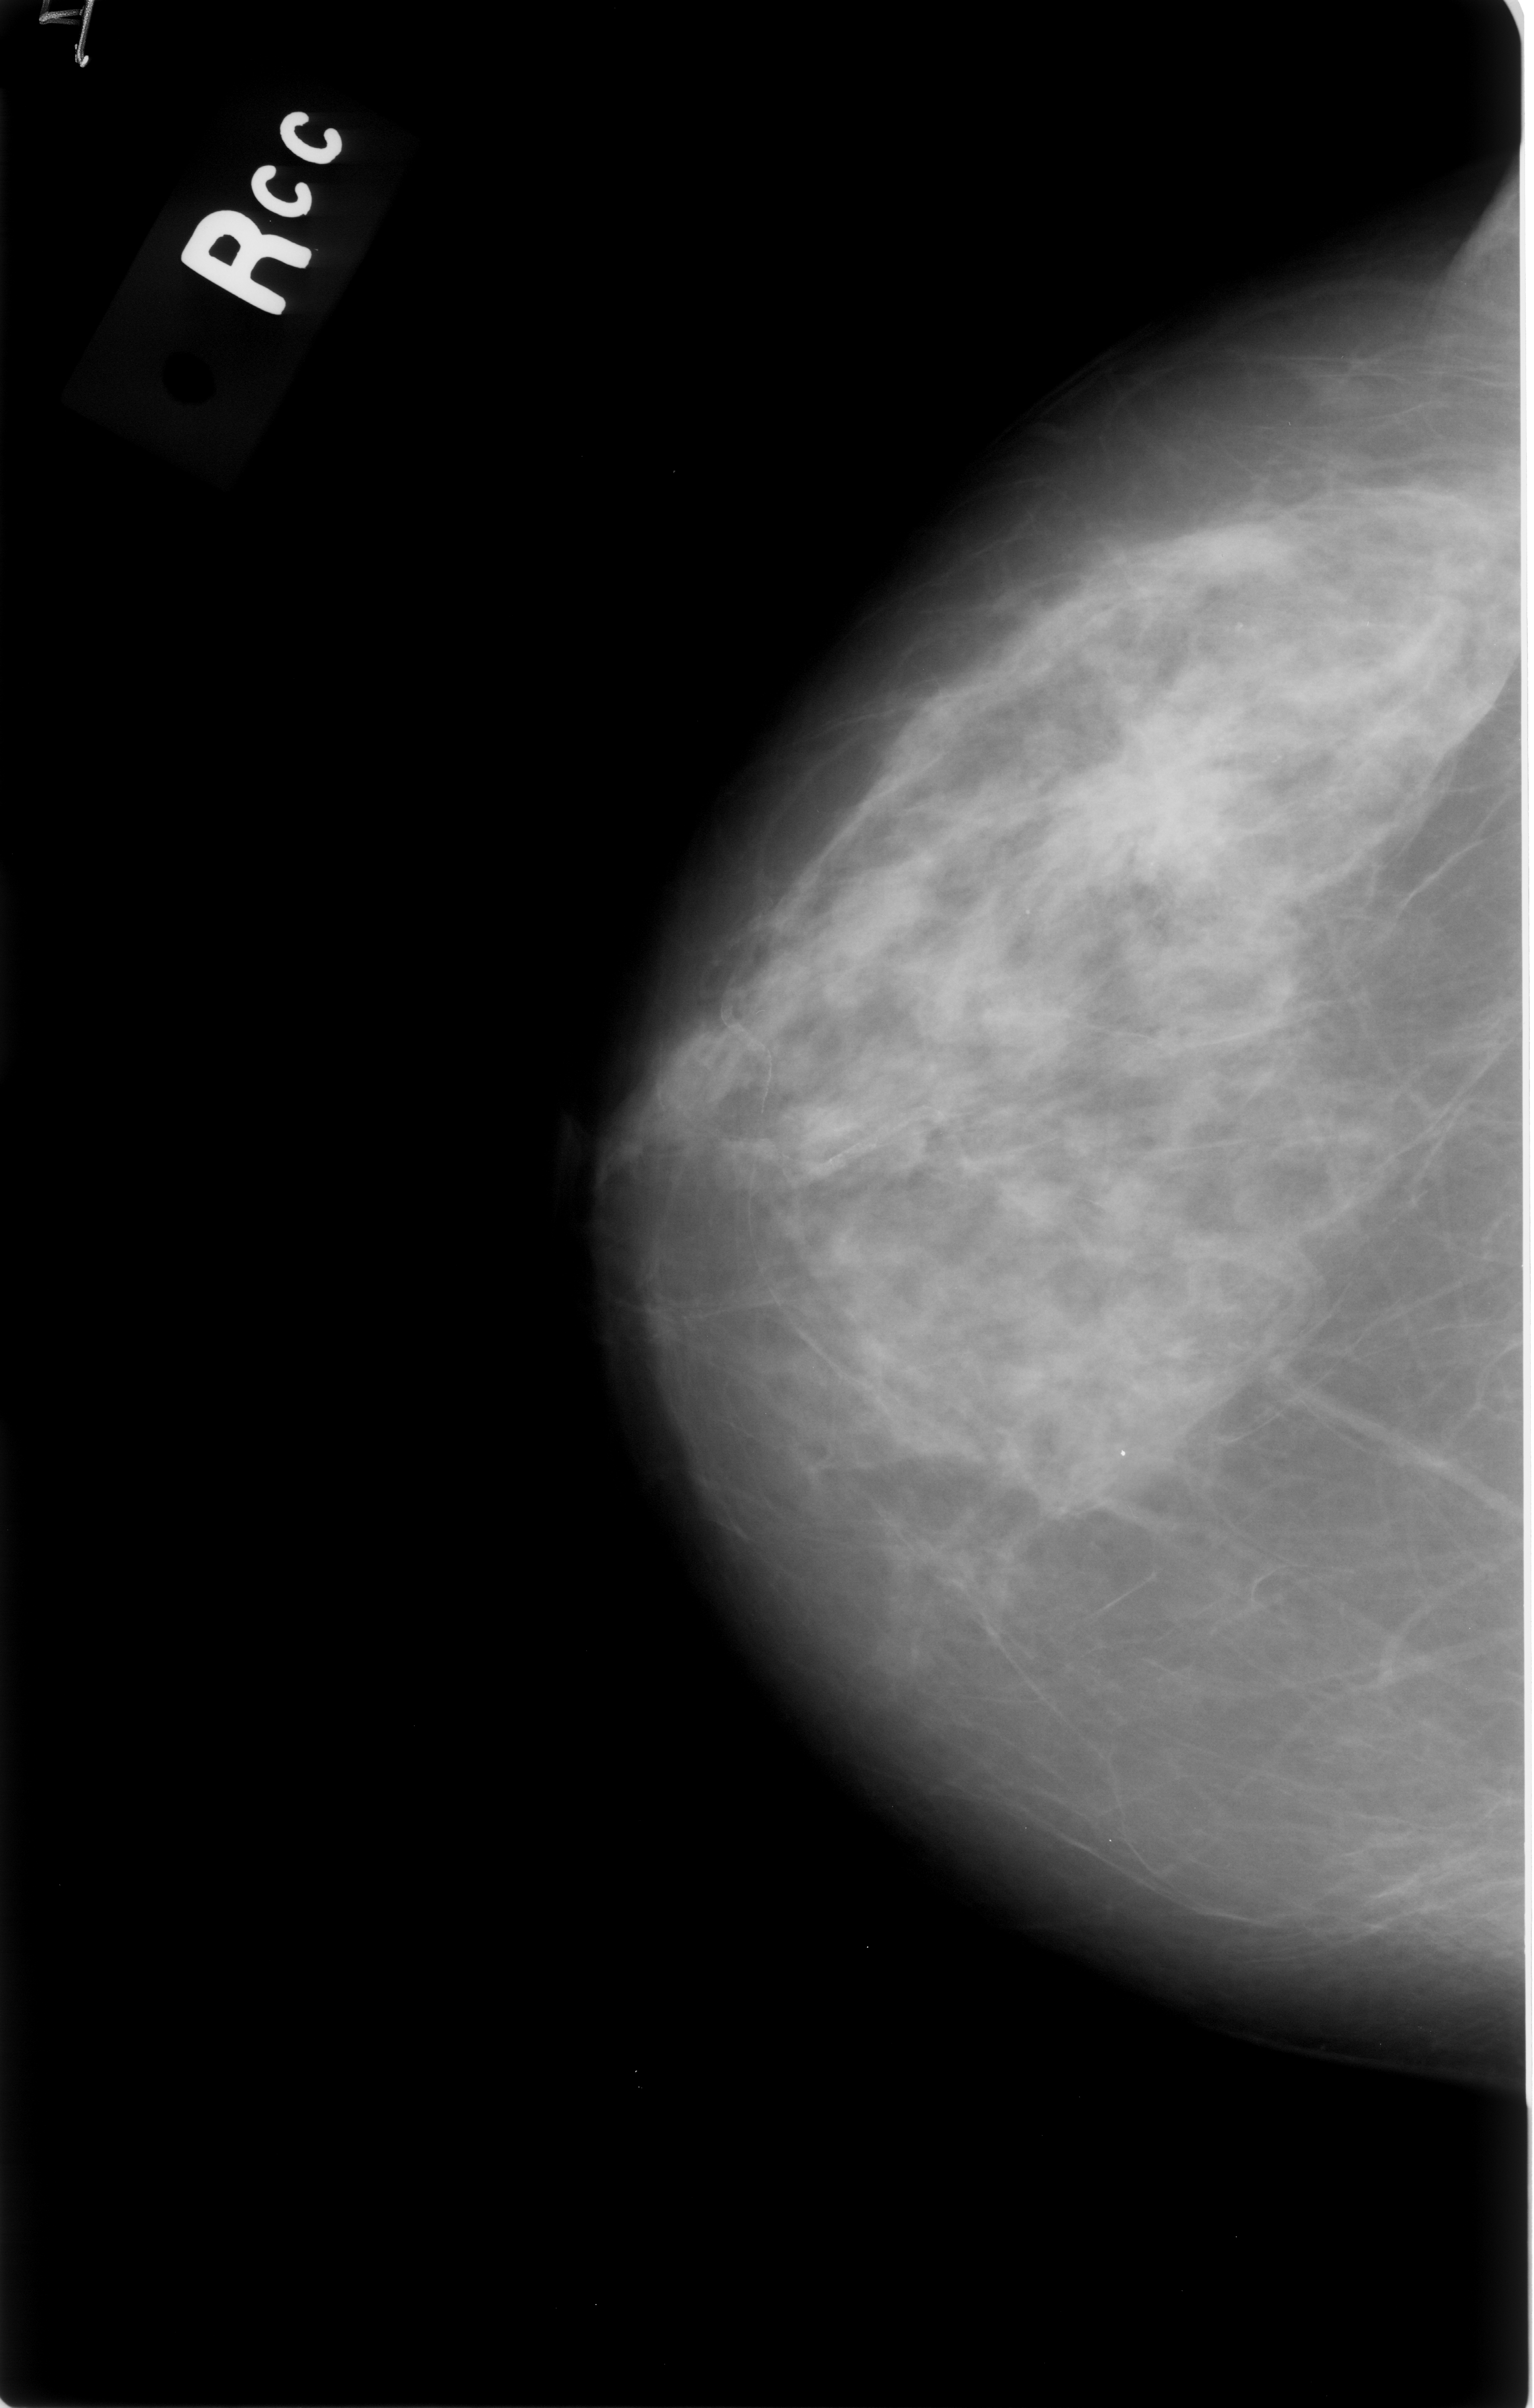
Digitized screen-film mammogram, right breast, craniocaudal (CC) view.
Mass, shape irregular, margins spiculated; BI-RADS assessment category 5; subtlety rating 5 on a 1 (subtle) to 5 (obvious) scale; pathology result (as recorded, not read from the image): malignant.